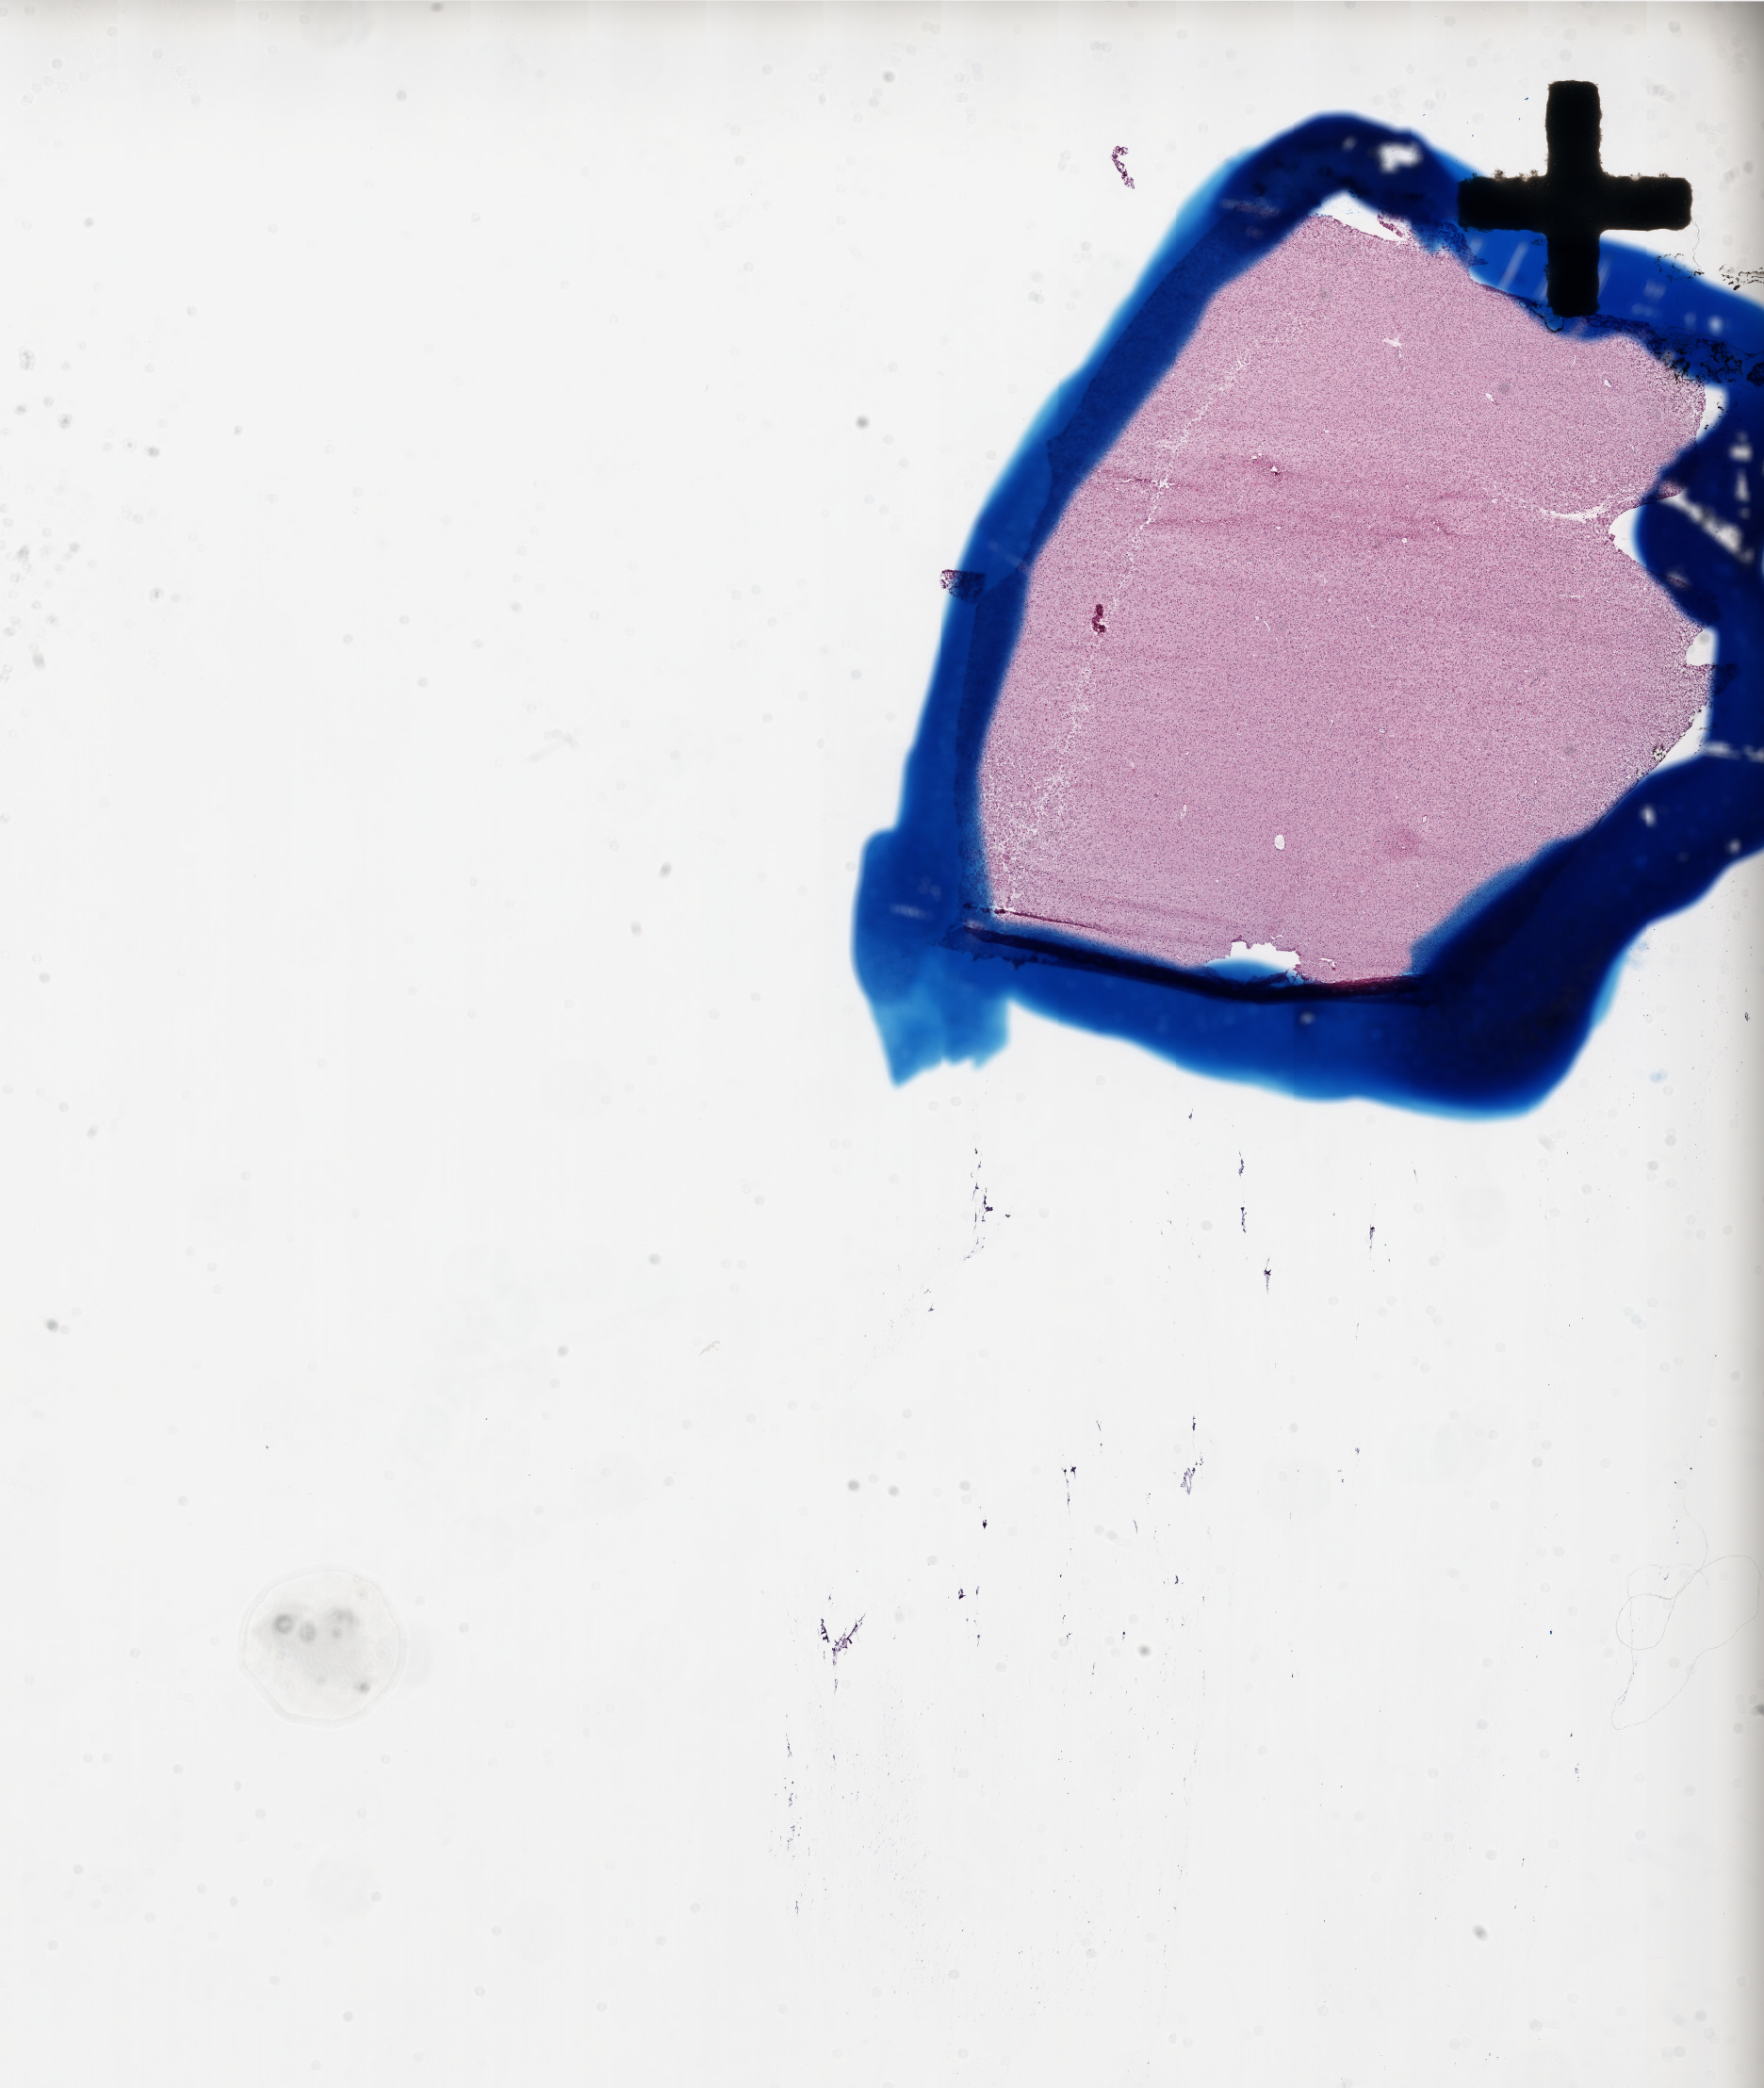
Digitized H&E tissue section (whole slide), low-resolution overview of the scanned area, about 15.0 x 17.7 mm (acquisition: 20x scan), frozen section, brain, primary tumour sample. Female patient; age at initial diagnosis 47 years. Slide review estimates, as recorded: tumour cells 100%, tumour nuclei 100%, normal cells 0%, stromal cells 0%, necrosis 0%. Infiltration values recorded for this section: lymphocyte infiltration 0%, neutrophil infiltration 0%.
Histologic diagnosis: Glioblastoma.